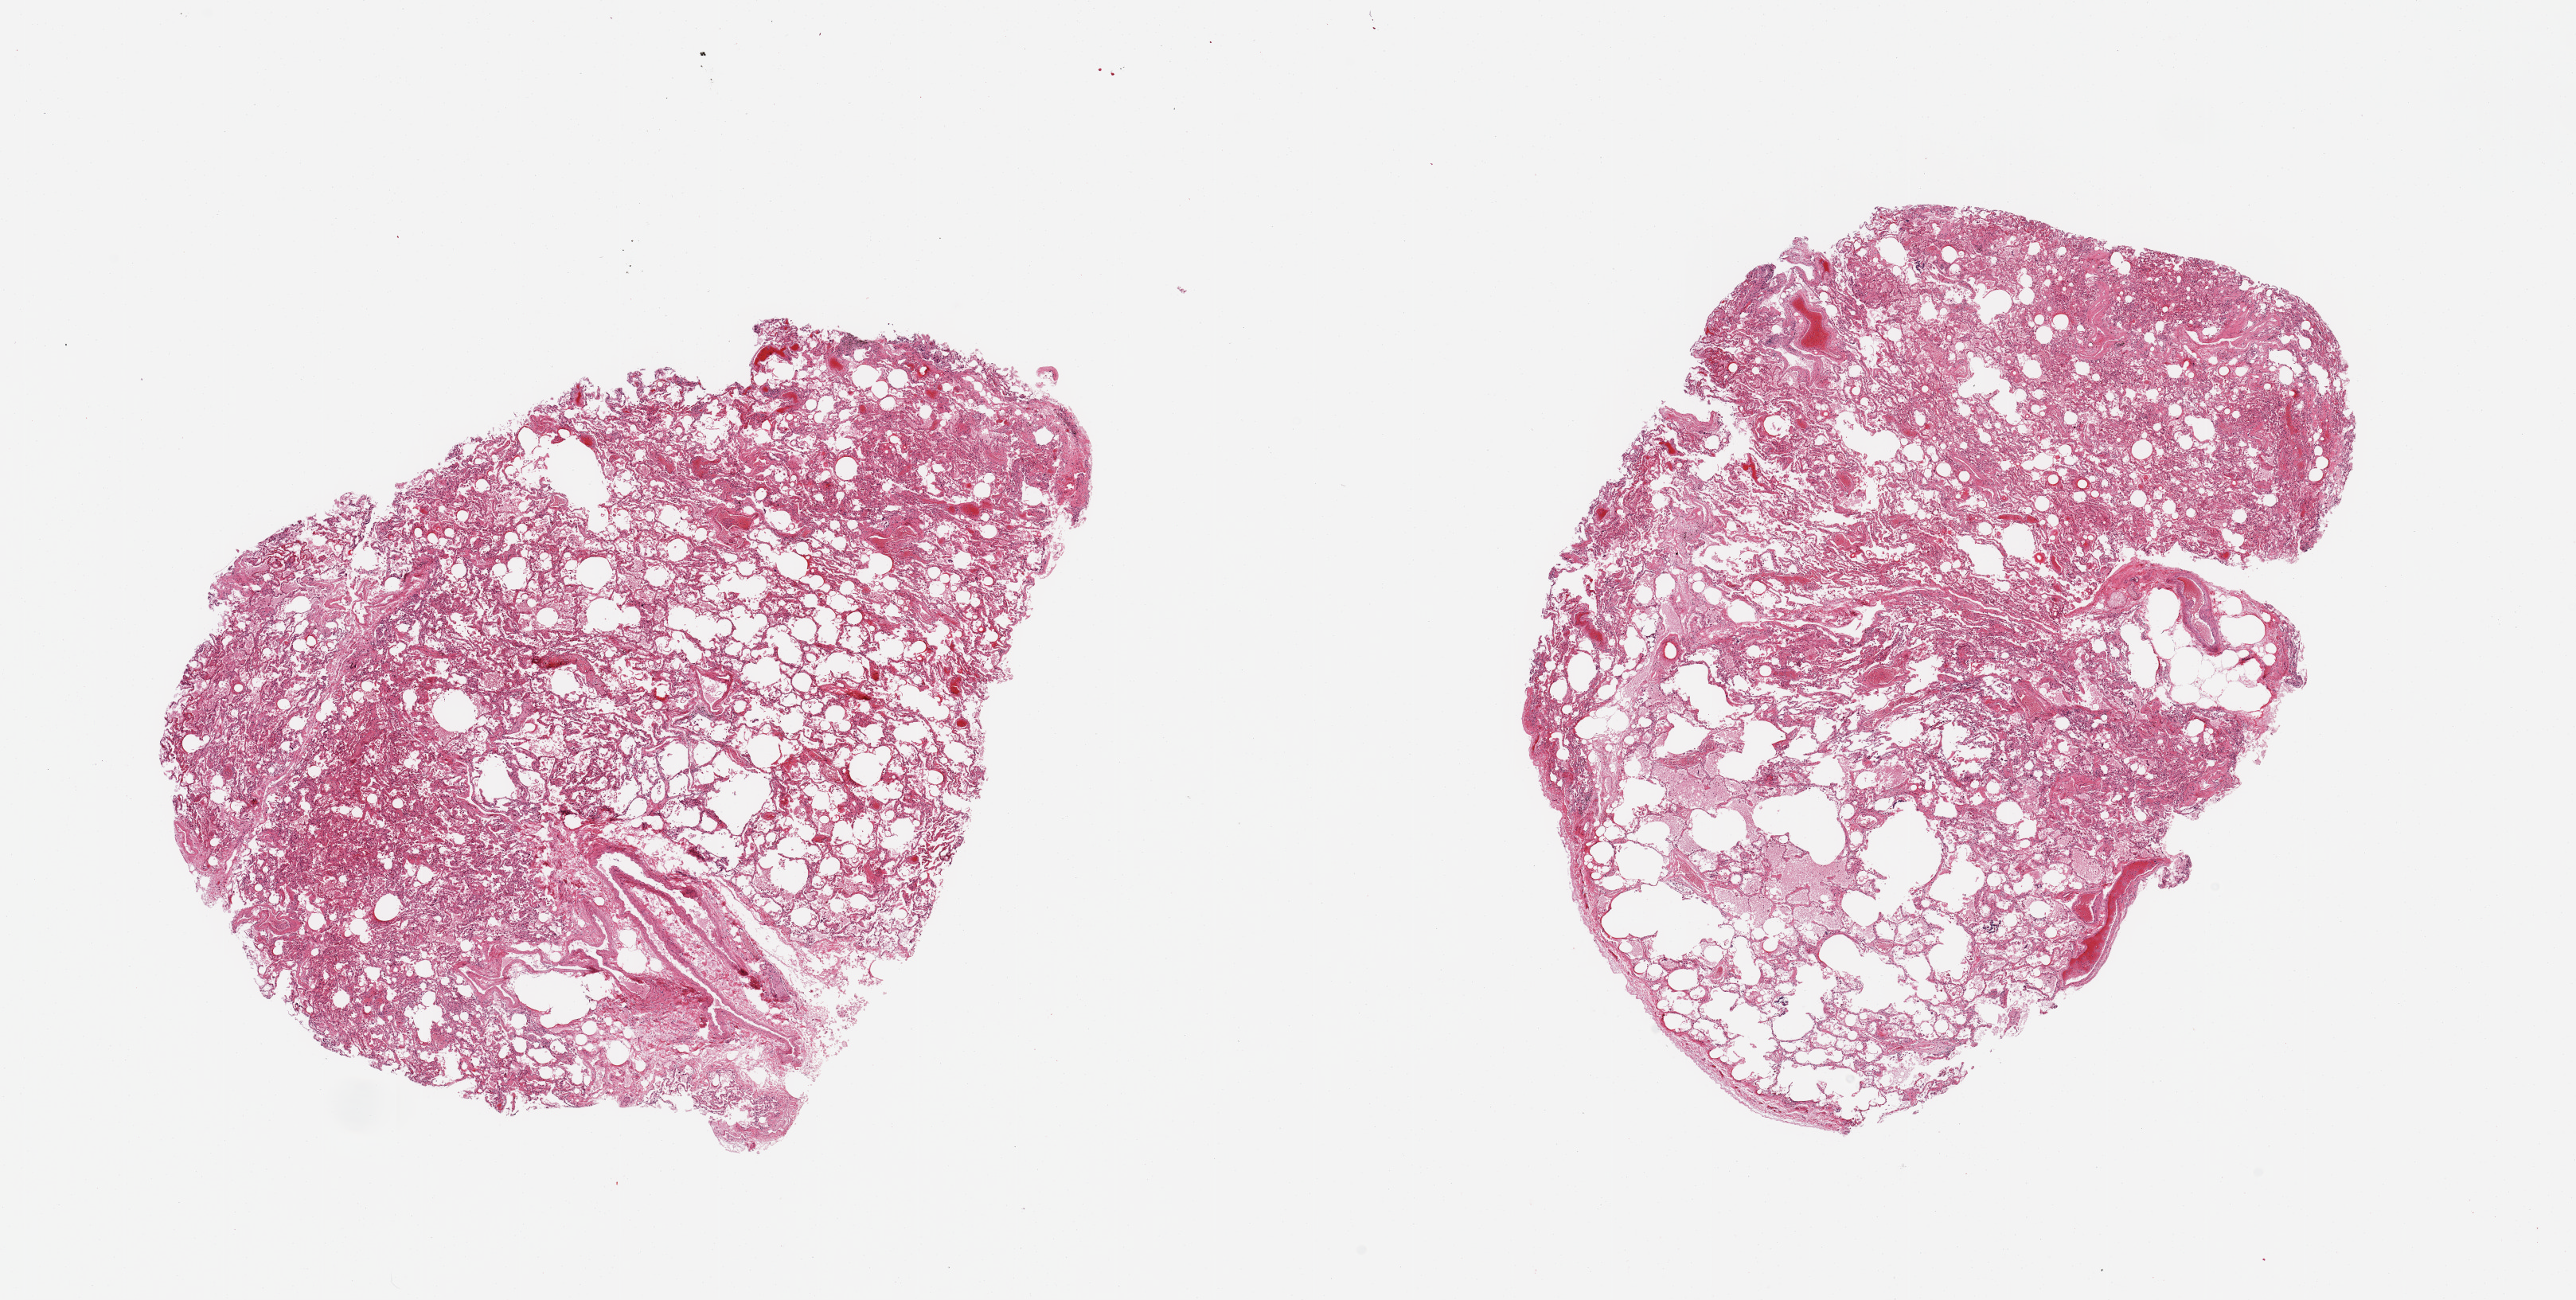
Digitized hematoxylin and eosin (H&E)-stained section, brightfield, low-resolution overview of the scanned area, about 25.6 x 12.9 mm (slide scanned at 20x); PAXgene-fixed, paraffin-embedded tissue; sampled site (target tissue): lung; tissue donor sample. Male donor.
Reviewer comment on this tissue sample: 2 pieces; includes portion of pleura (not target region), some collapse, some widened airspaces, congestion, edema.